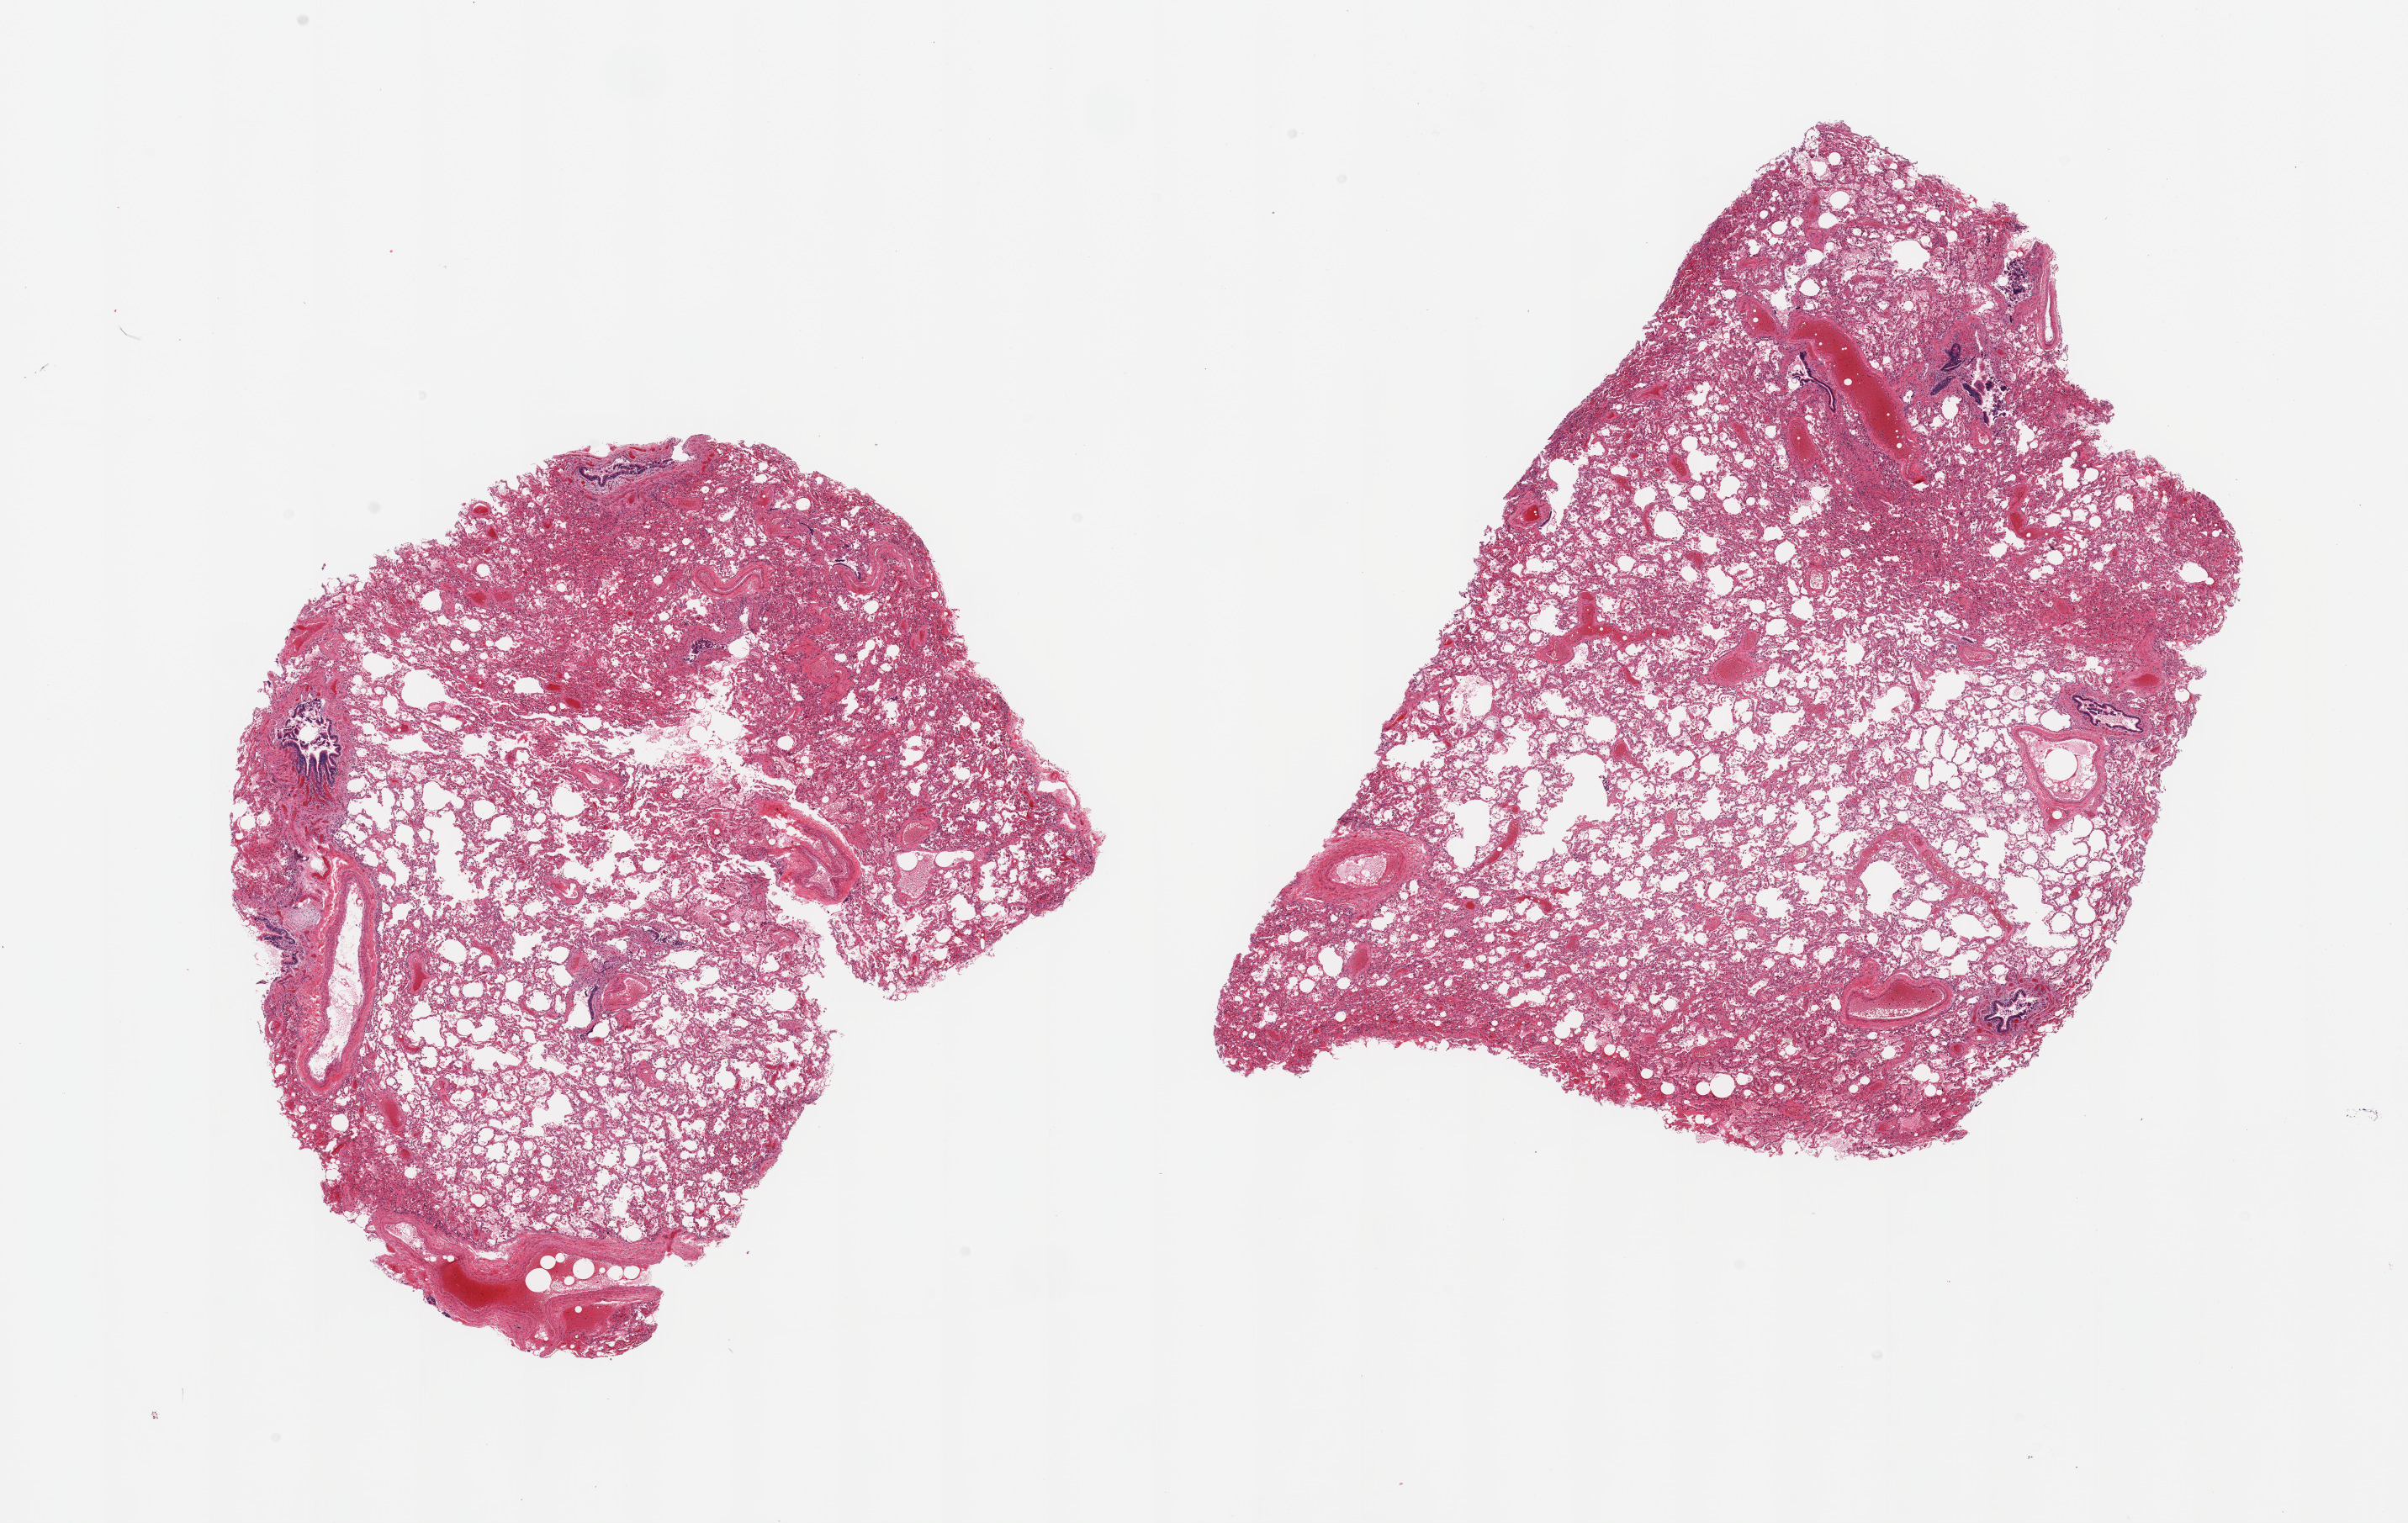
Haematoxylin and eosin whole-slide image, low-resolution overview of the scanned area, about 22.6 x 14.3 mm (acquisition: 20x scan); PAXgene-fixed paraffin-embedded (PFPE) section; sampled site (target tissue): lung; tissue donor sample. Donor: male.
• review note (as recorded): 2 pieces, mild congestion